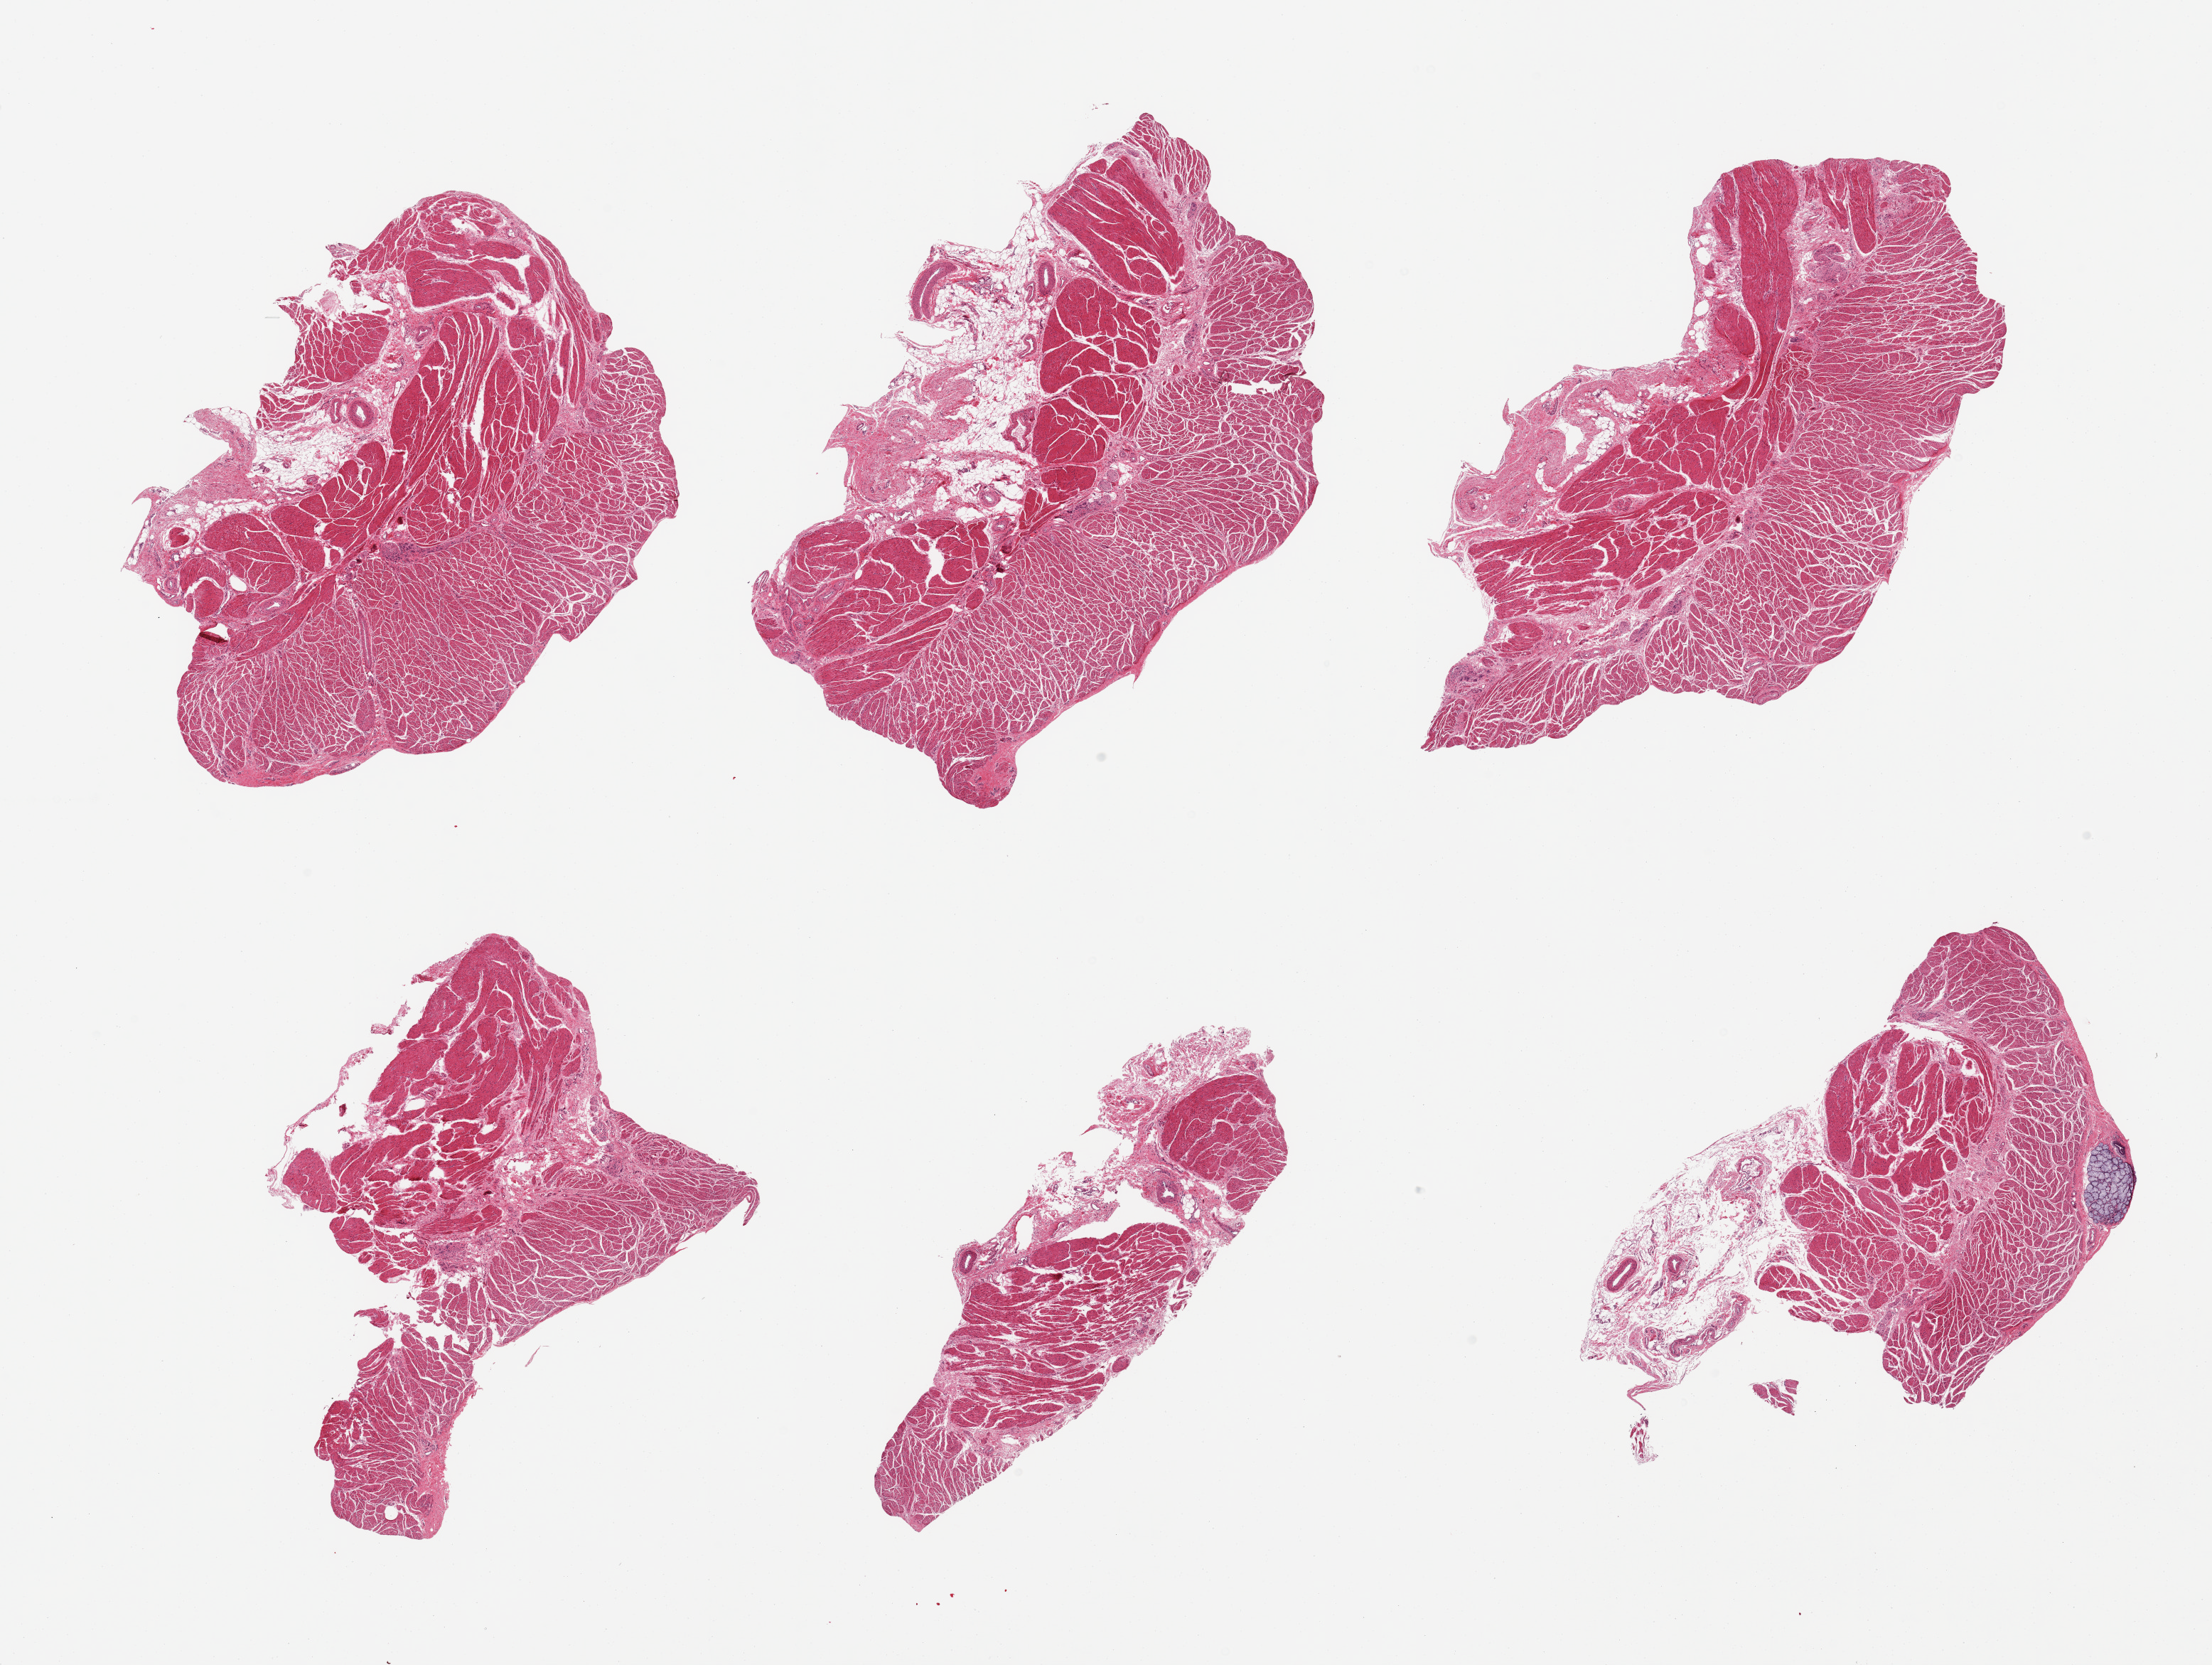
Digitized hematoxylin and eosin (H&E)-stained section — whole scanned area (about 24.6 x 18.5 mm, acquisition: 20x scan) shown as a low-resolution overview; PAXgene-fixed, paraffin-embedded tissue; sampled site (target tissue): gastroesophageal junction; tissue donor sample. Male donor.
Pathologist's review note for this sample: 6 pieces; target muscularis present with attached fat/vessels and focal mucus glands.